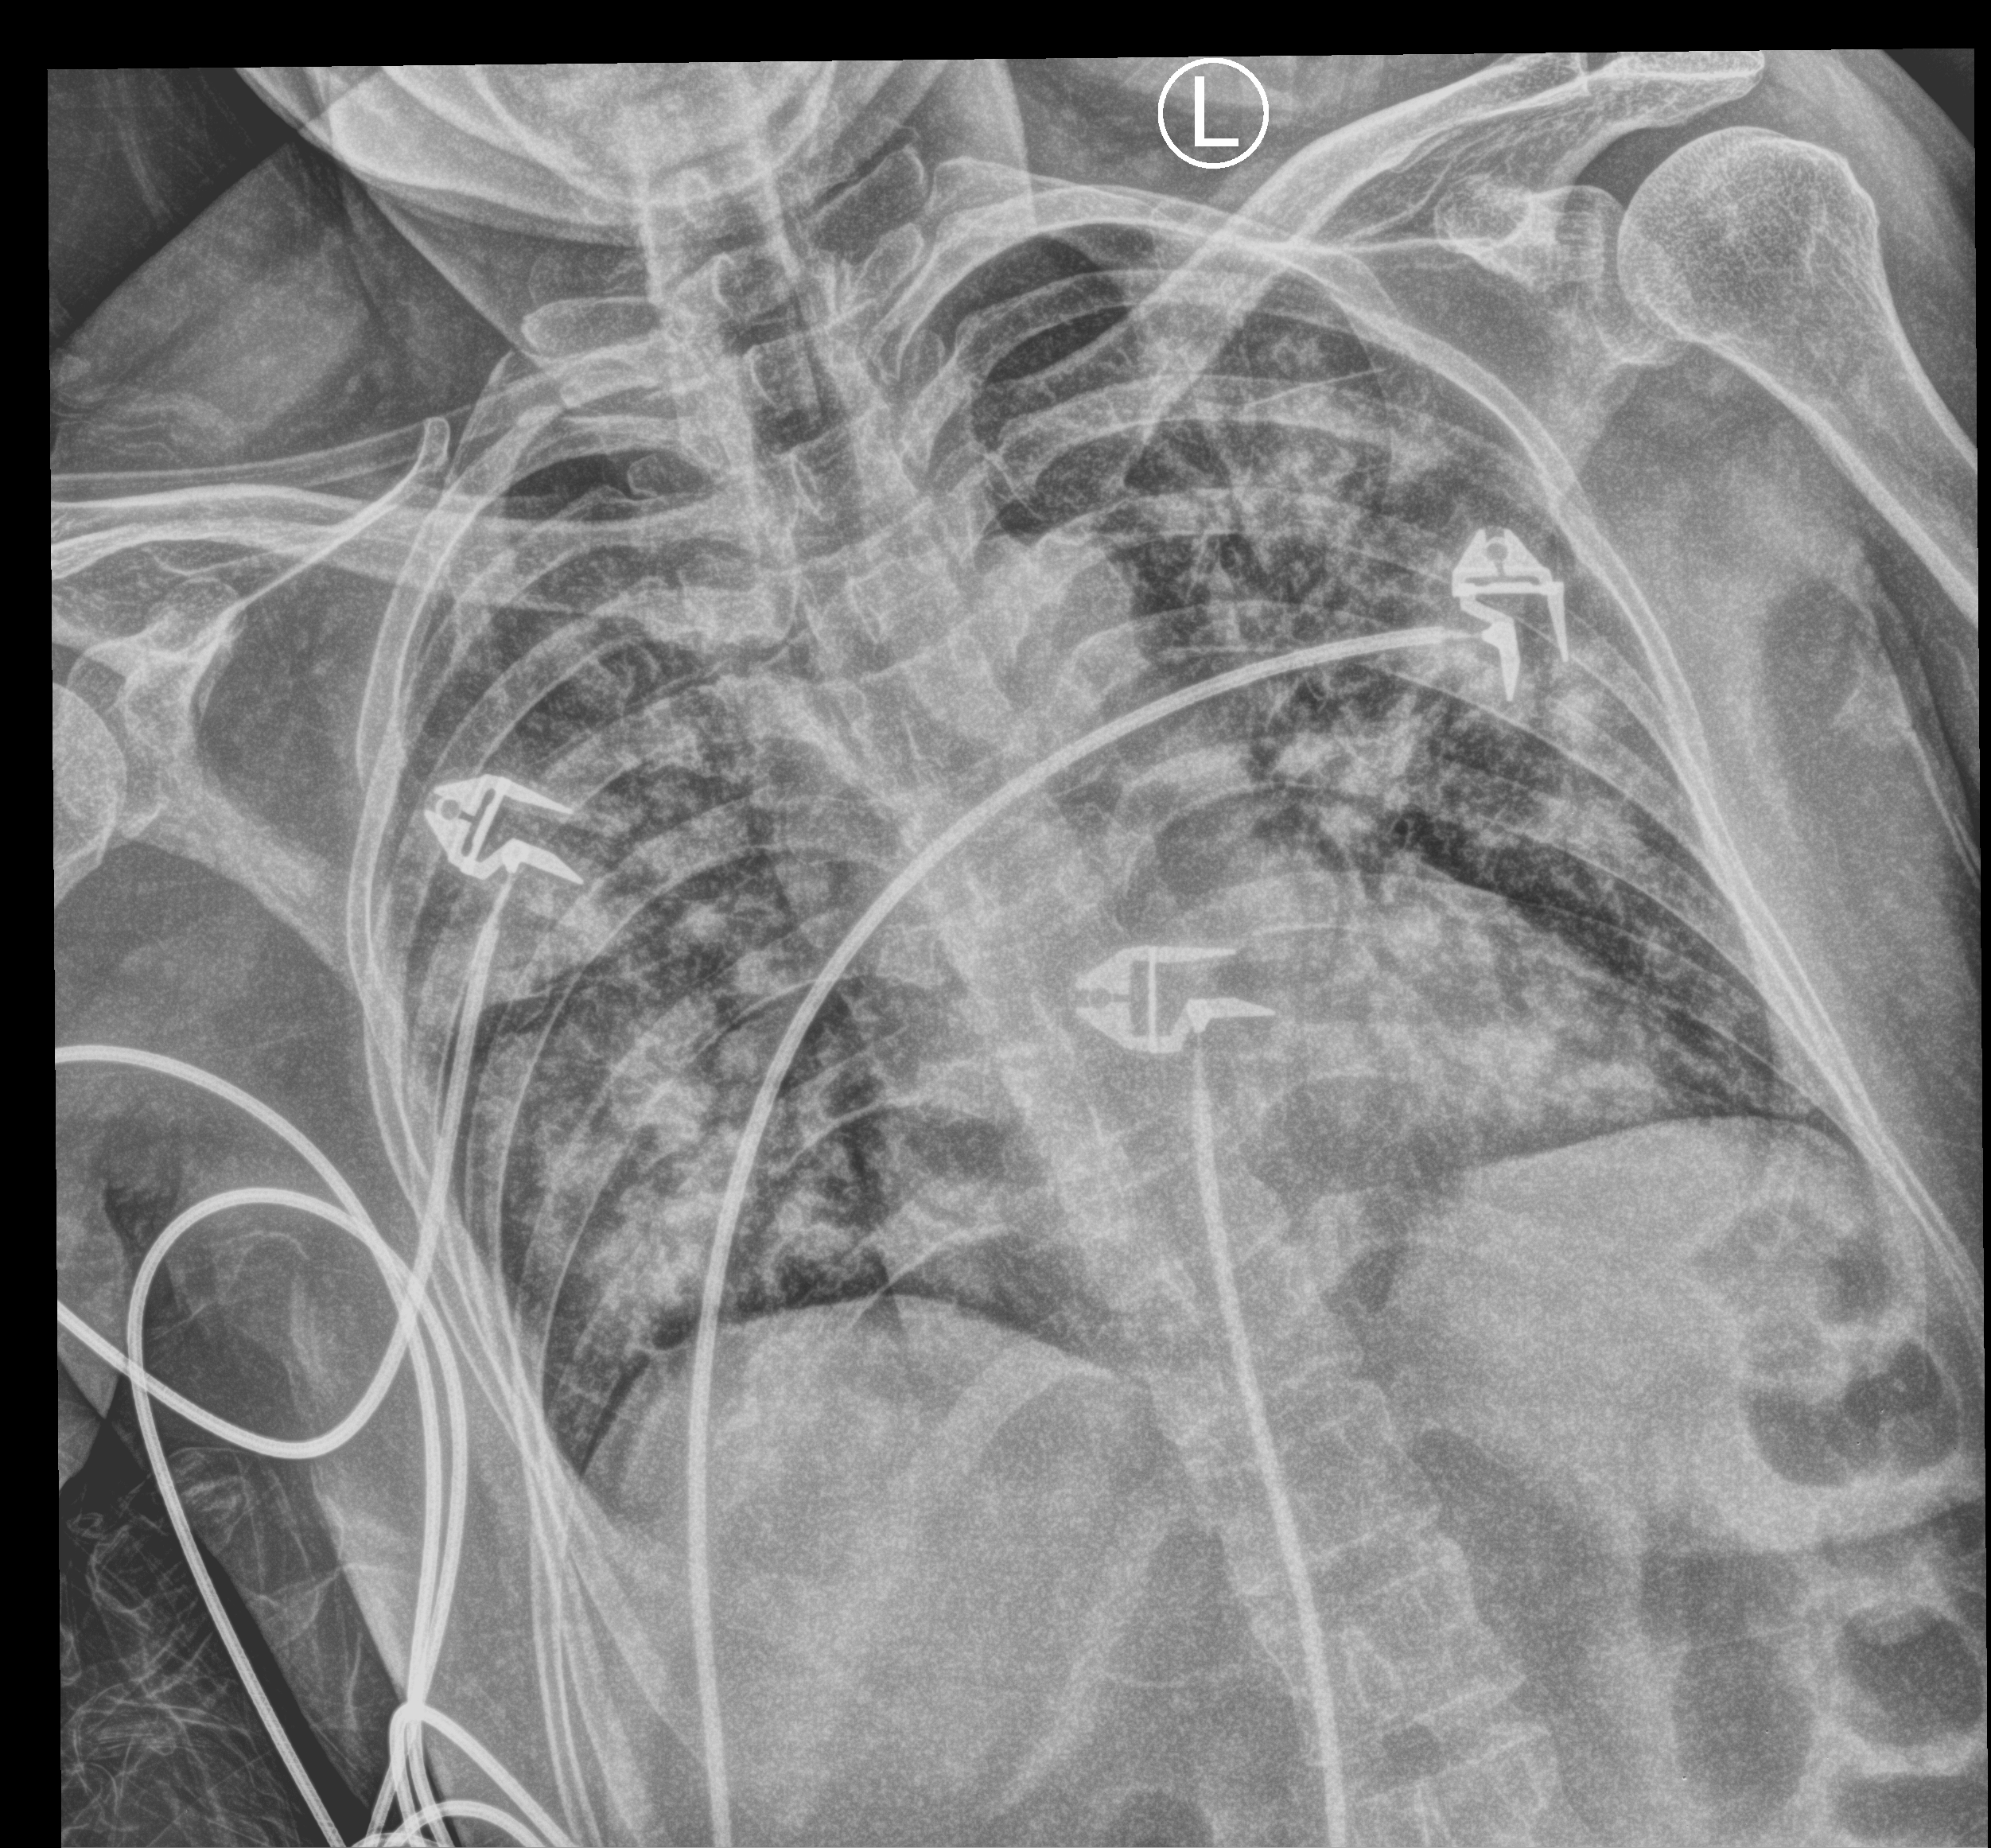
Chest X-ray (portable), anteroposterior (AP) projection. Patient hospitalised with COVID-19; female, aged 60–74 years.
From the hospital-stay record, not from the radiograph (when in the stay this image was taken is not recorded):
- COPD (admission record): no
- mechanically ventilated during this hospital stay: yes